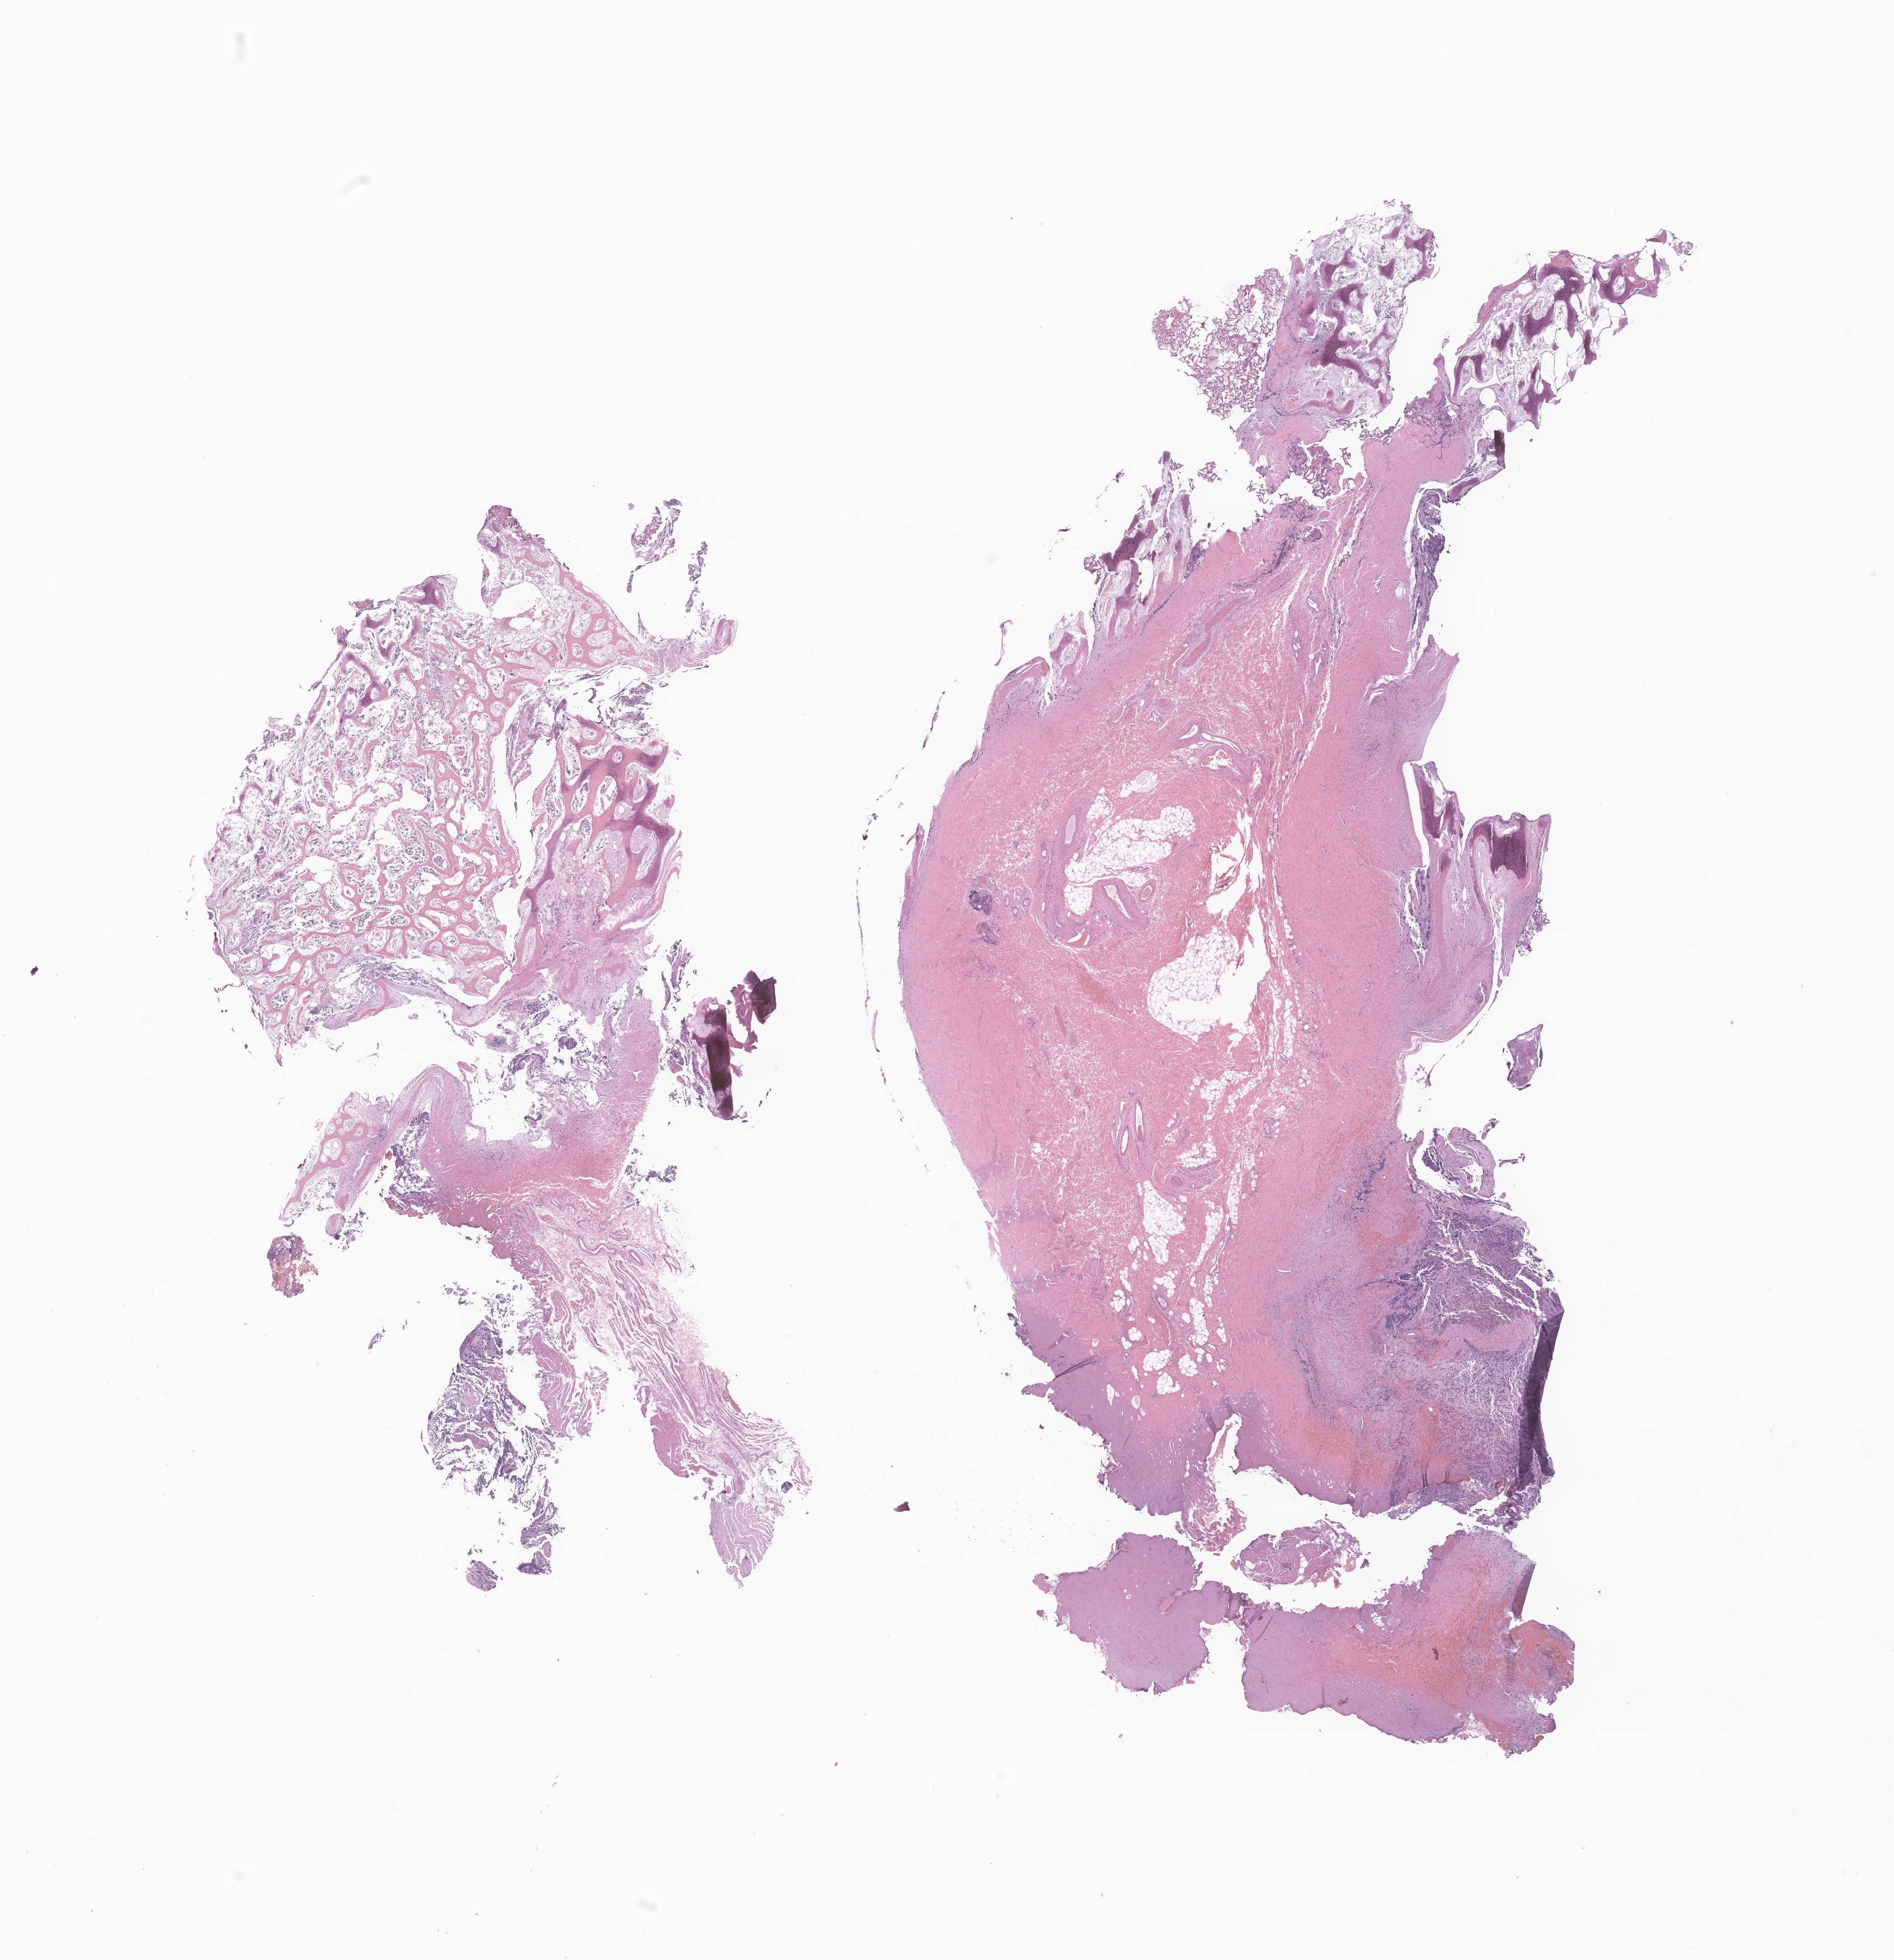
Whole-slide image, H&E stain of tumor tissue from the orbit — a low-resolution overview of the entire scanned area, about 17.7 x 18.3 mm; formalin-fixed, paraffin-embedded (FFPE) tissue. Male patient, age 191 days.
Recorded diagnosis: Neuroblastoma, NOS.